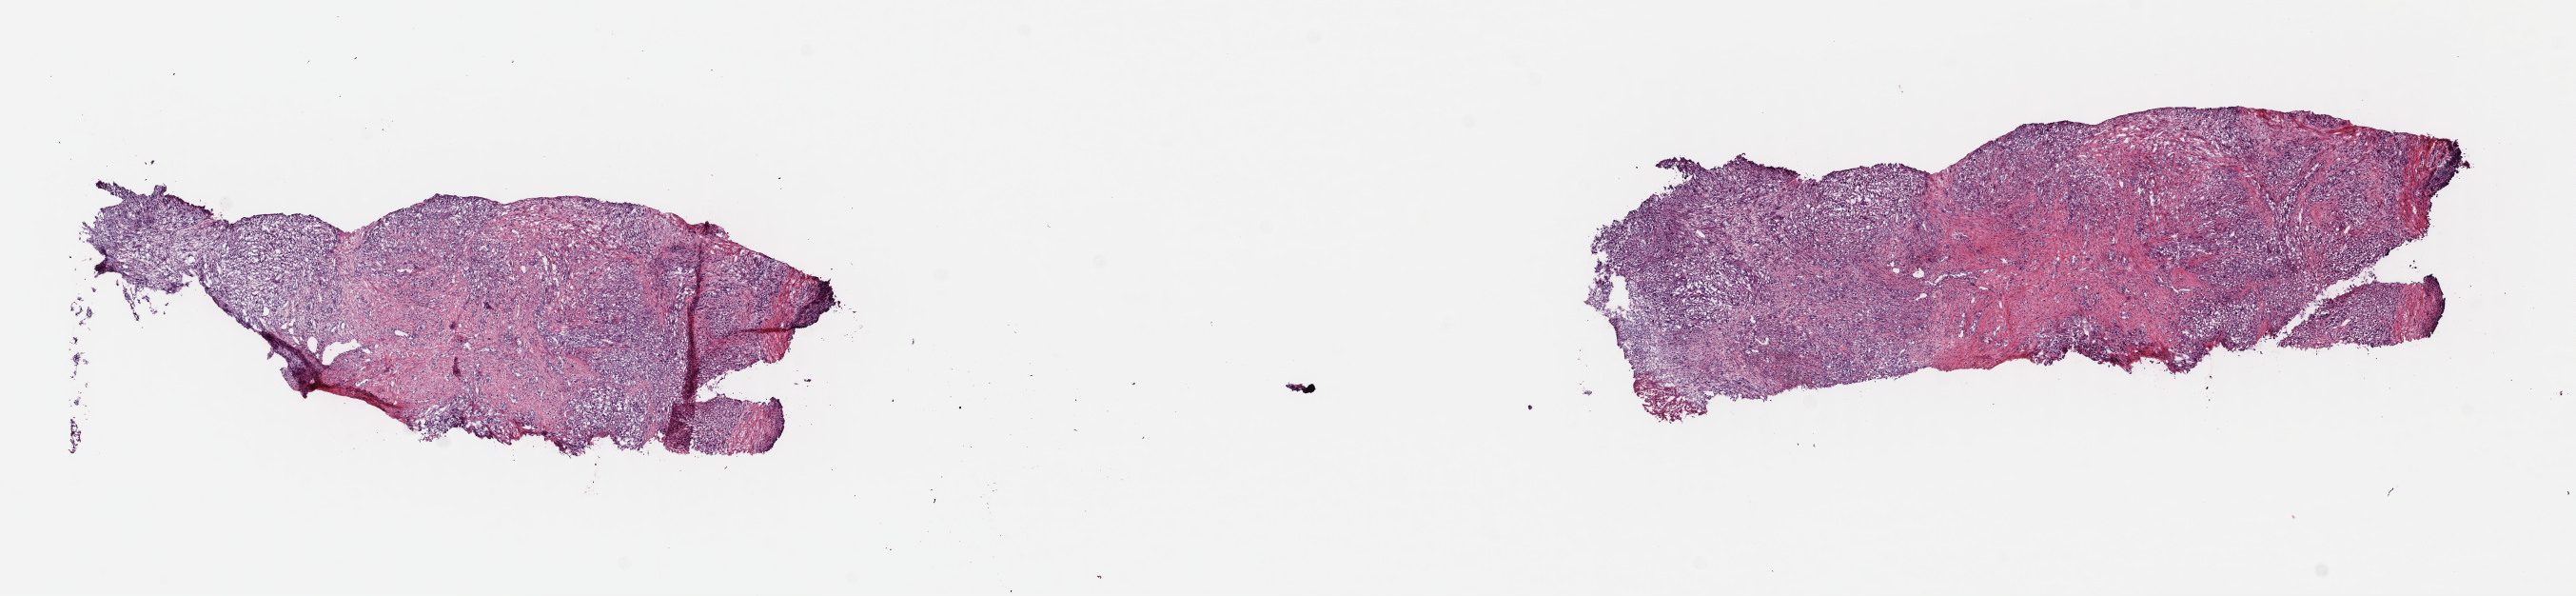
H&E whole-slide image, a low-resolution overview of the entire scanned area, about 21.3 x 4.9 mm (slide scanned at 40x). Frozen section from the top of the tissue portion. Metastatic tumour sample, sampled site not recorded. Male patient; age at initial diagnosis 23 years. Slide review estimates, as recorded: tumour cells 100%, tumour nuclei 80%, normal cells 0%, stromal cells 0%, necrosis 0%. Inflammatory infiltration, as recorded: lymphocyte infiltration 0%, monocyte infiltration 0%, neutrophil infiltration 0%.
• this section: metastatic tumour tissue
• patient diagnosis: Malignant melanoma, NOS